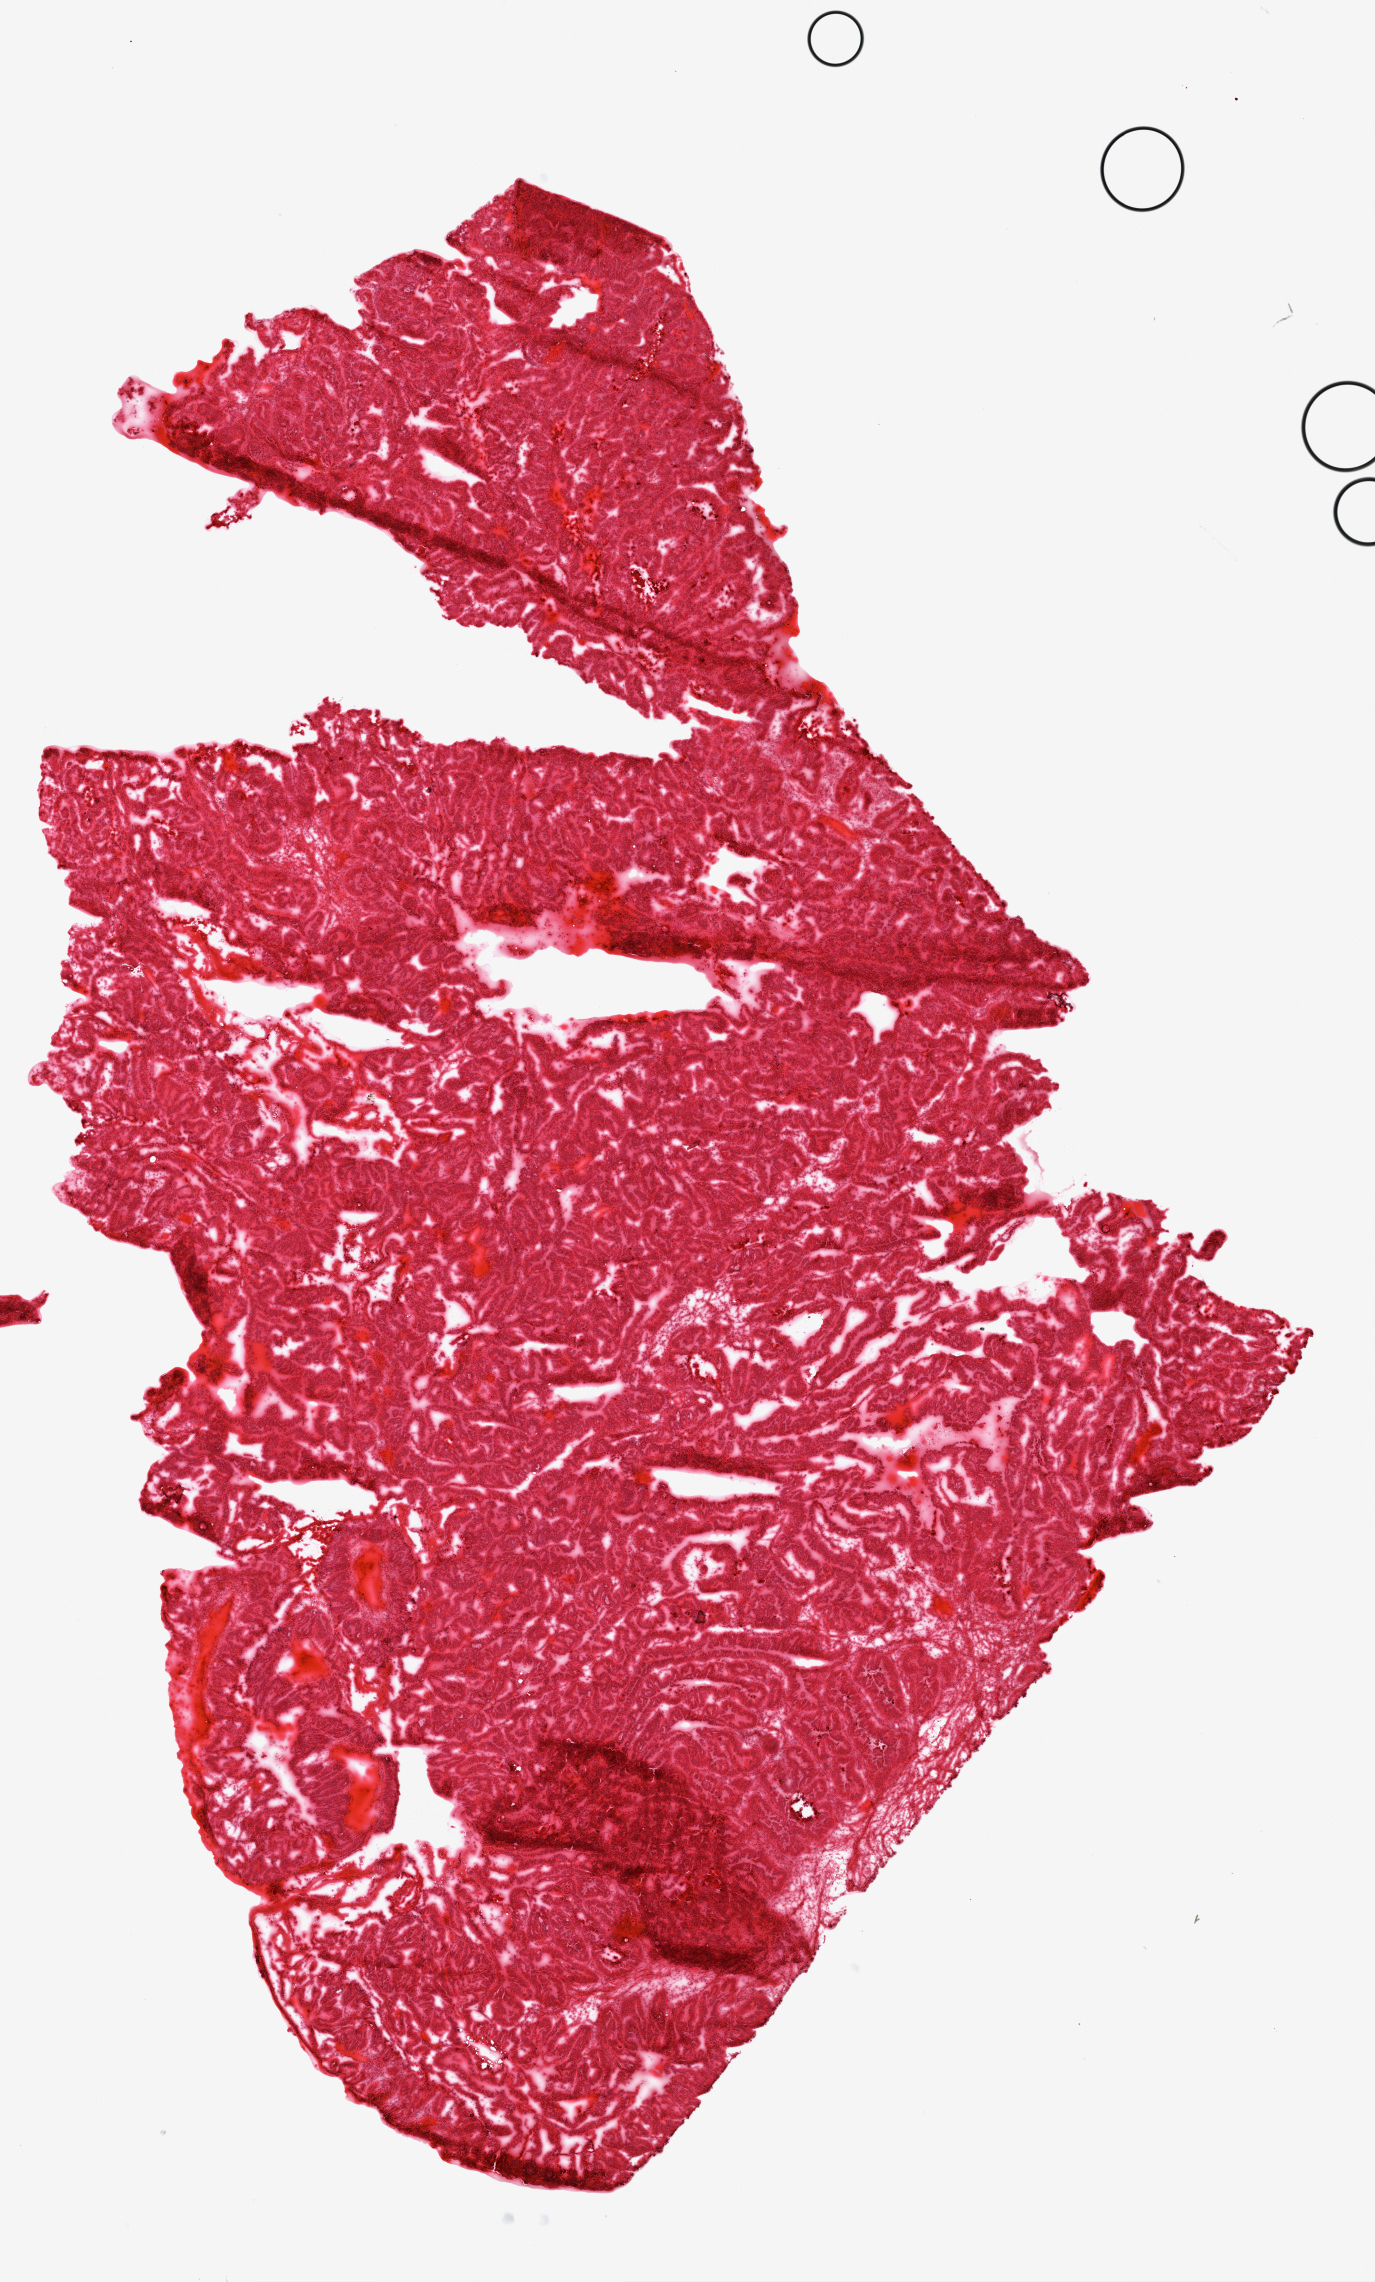
Digitized H&E tissue section (whole slide), low-resolution overview of the scanned area, about 11.0 x 18.3 mm (slide scanned at 20x); frozen section from the top of the tissue portion; ovary, primary tumour sample. Female patient; age at initial diagnosis 51 years. Histologic grade: G4 (undifferentiated). Composition of this section per pathologist review: tumour cells 98%, tumour nuclei 95%, normal cells 0%, stromal cells 2%, necrosis 0%.
FIGO stage: IIIC. Diagnosis: Serous cystadenocarcinoma, NOS.